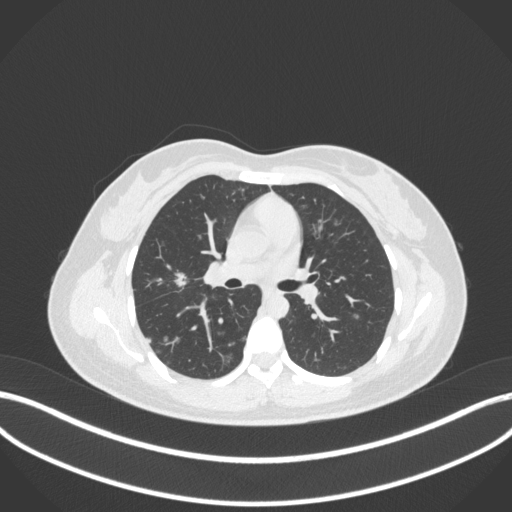
Chest CT, one axial slice; slice 195 of 214 in the series (ordered by position); reconstruction kernel B31f; lung window (W 1500 / L -600 HU); 1 mm slice thickness; 512 × 512 image matrix. Patient: female, 33 years. From the clinical record (not read from this slice): clinical TNM (as recorded): T1c N0 M0.
Outlined on this slice (rectangle marked by the reading radiologist):
- lung tumour (recorded histology: adenocarcinoma): bounding box (x1, y1, x2, y2) in pixels: (172, 270, 188, 289)